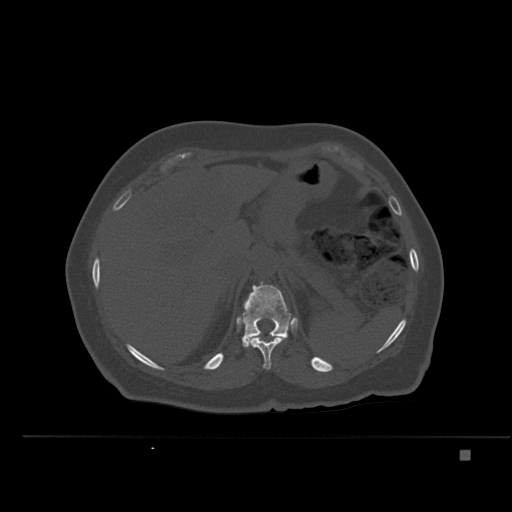
CT including the spine, one axial slice. Position 260 of 477 along the scan axis. Bone window (W 1800 / L 400 HU). 1.5 mm slice thickness. 512 × 512 image matrix, field of view 422 × 422 mm. Female patient, age 74 years. From the clinical record (not read from this slice): primary cancer: colon.
Annotated regions visible in this slice (semi-automatically segmented with operator editing):
- T11 vertebra: bounding box <248,335,284,369> (left, top, right, bottom; pixels)
- T12 vertebra: <242,282,294,347>